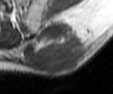
MRI of an extremity soft-tissue mass, one axial slice. Position 24 of 42 along the scan axis. MR volume resampled by the dataset authors to the PET/CT grid (not the native acquisition matrix). 3.27 mm slice thickness. 113 × 94 image matrix. Male patient. From the clinical record (not read from this slice): histological type: leiomyosarcoma; grade: intermediate; site of the primary tumour: left pelvis.
Annotated regions visible in this slice (expert contour drawn on MRI and transferred to this co-registered scan by the dataset authors):
- gross tumour volume (mass): bounding box [x1, y1, x2, y2] px = [24, 18, 91, 72]